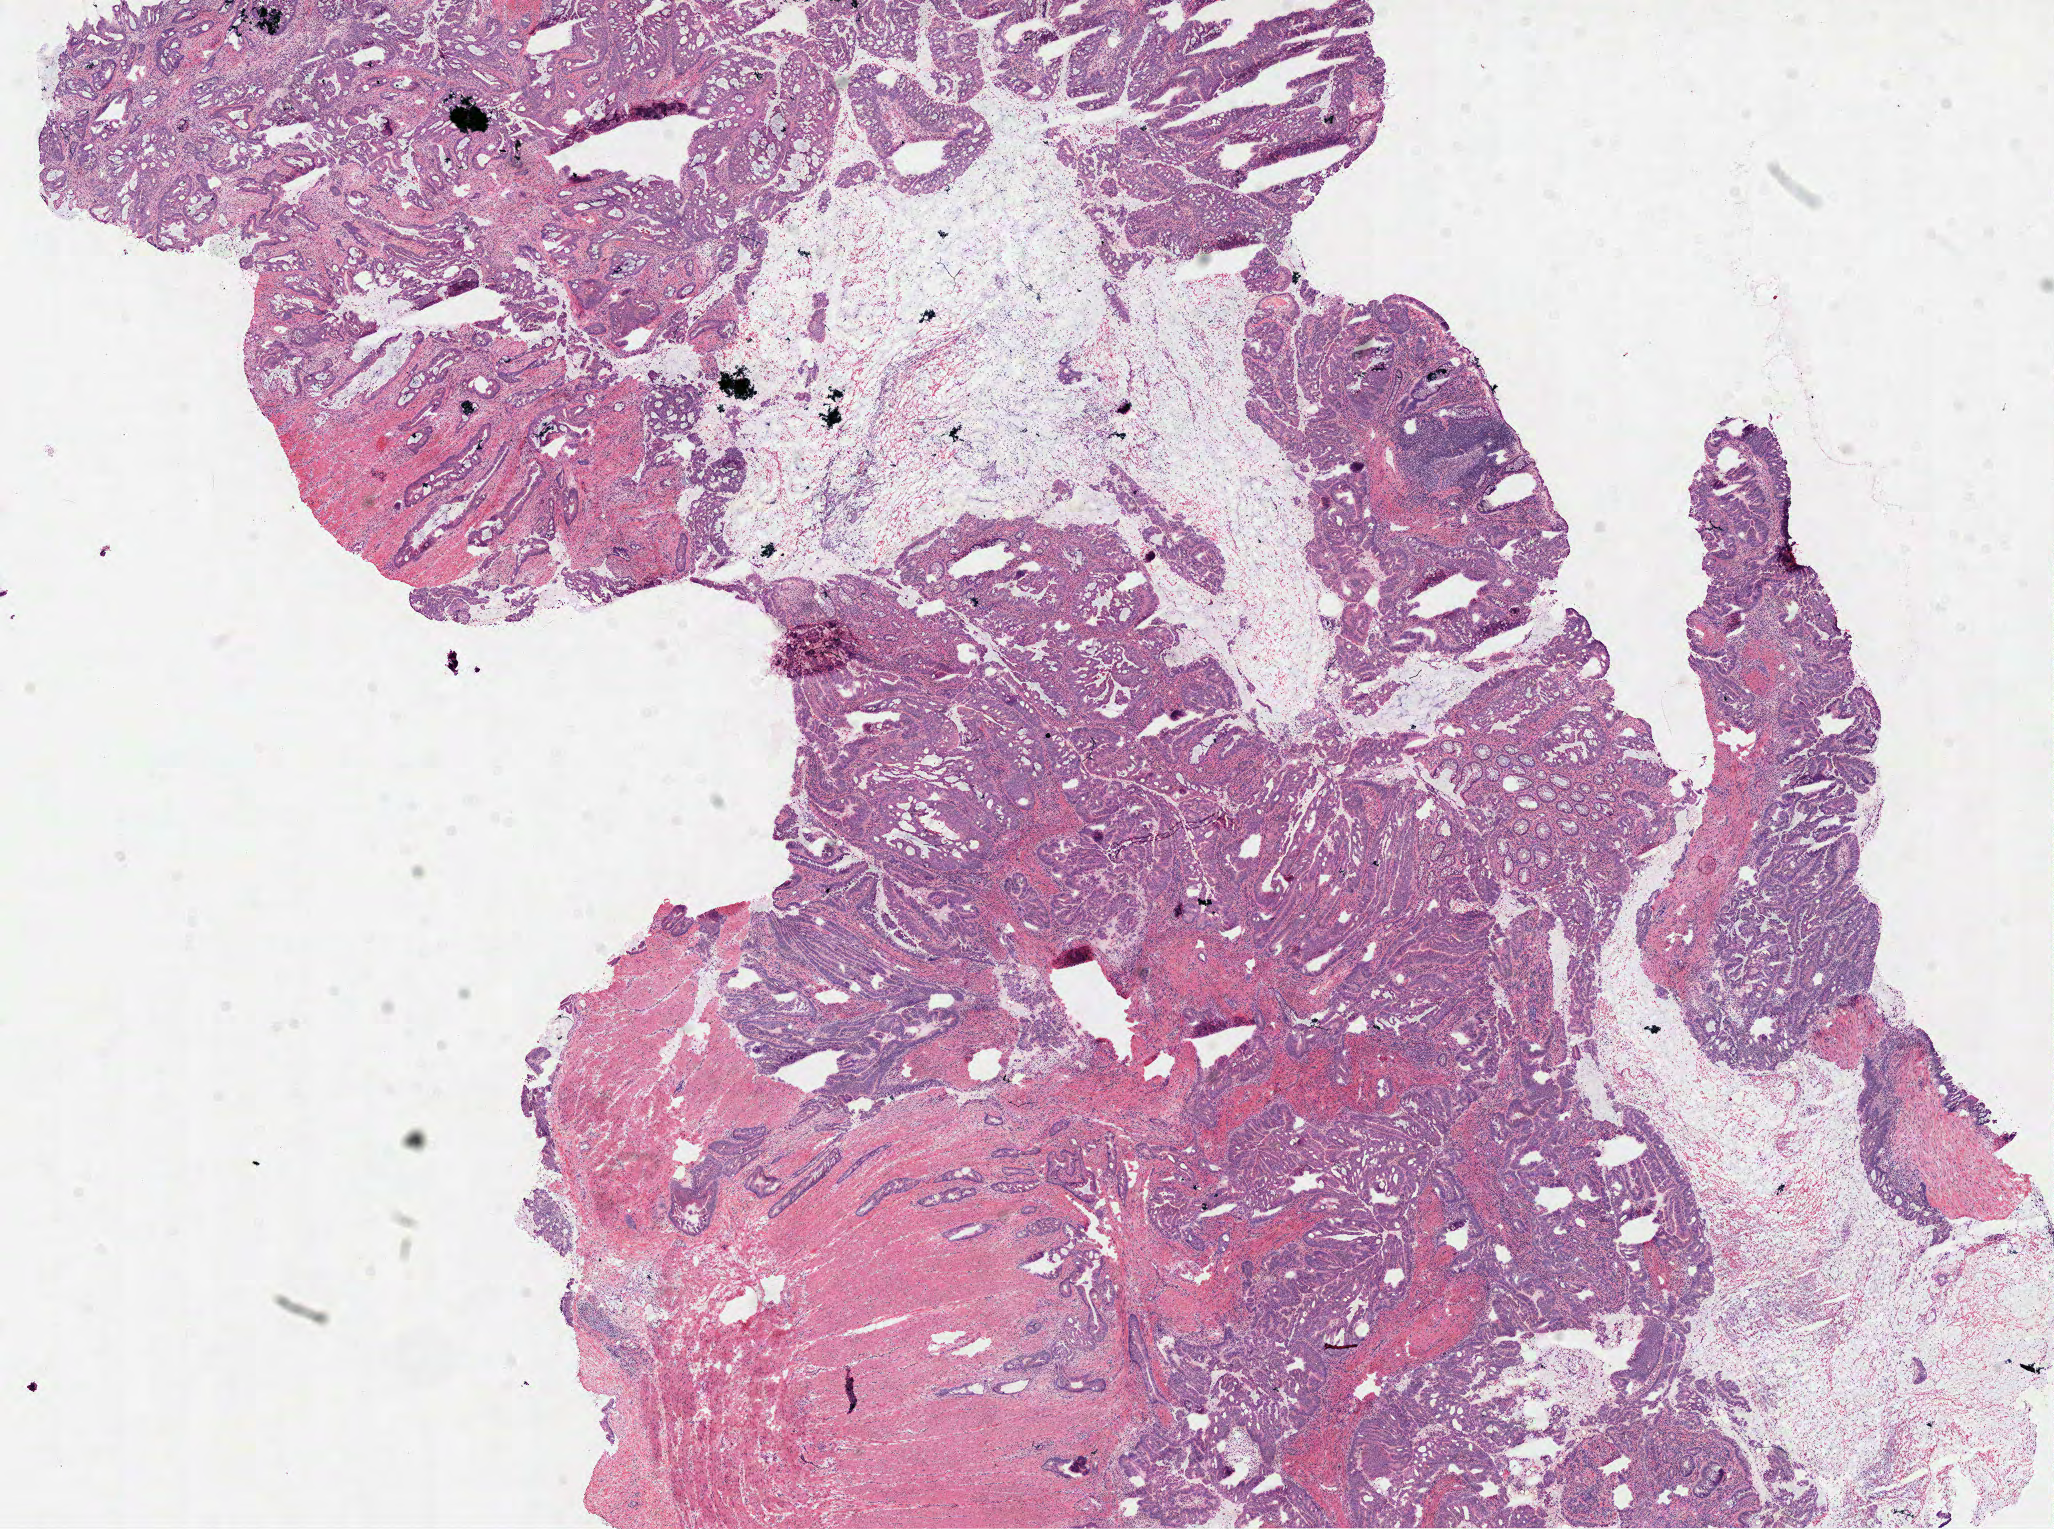
Hematoxylin and eosin (H&E) stained whole-slide image, shown as a low-resolution overview of the whole scanned area (about 16.6 x 12.3 mm, slide scanned at 40x), frozen section from the top of the tissue portion, rectum, primary tumour sample. Female, age 70 years at initial diagnosis.
Diagnosis: Adenocarcinoma, NOS (rectosigmoid junction).